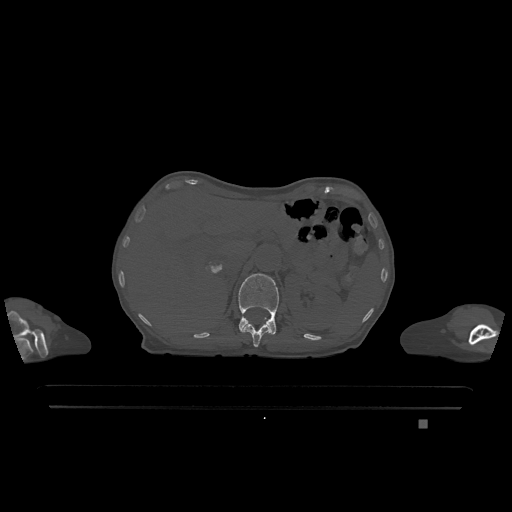
CT including the spine, one axial slice. Slice 499 of 1317 in the series (ordered by position). Bone window (W 1800 / L 400 HU). 512 × 512 image matrix, field of view 500 × 500 mm. Female patient, age 74 years. From the clinical record (not read from this slice): primary cancer: lung.
Structures marked on this image (semi-automatic segmentation, software-assisted and operator-edited):
- L1 vertebra: bounding box [x1, y1, x2, y2] px = [238, 273, 279, 335]
- T12 vertebra: [242, 318, 270, 347]